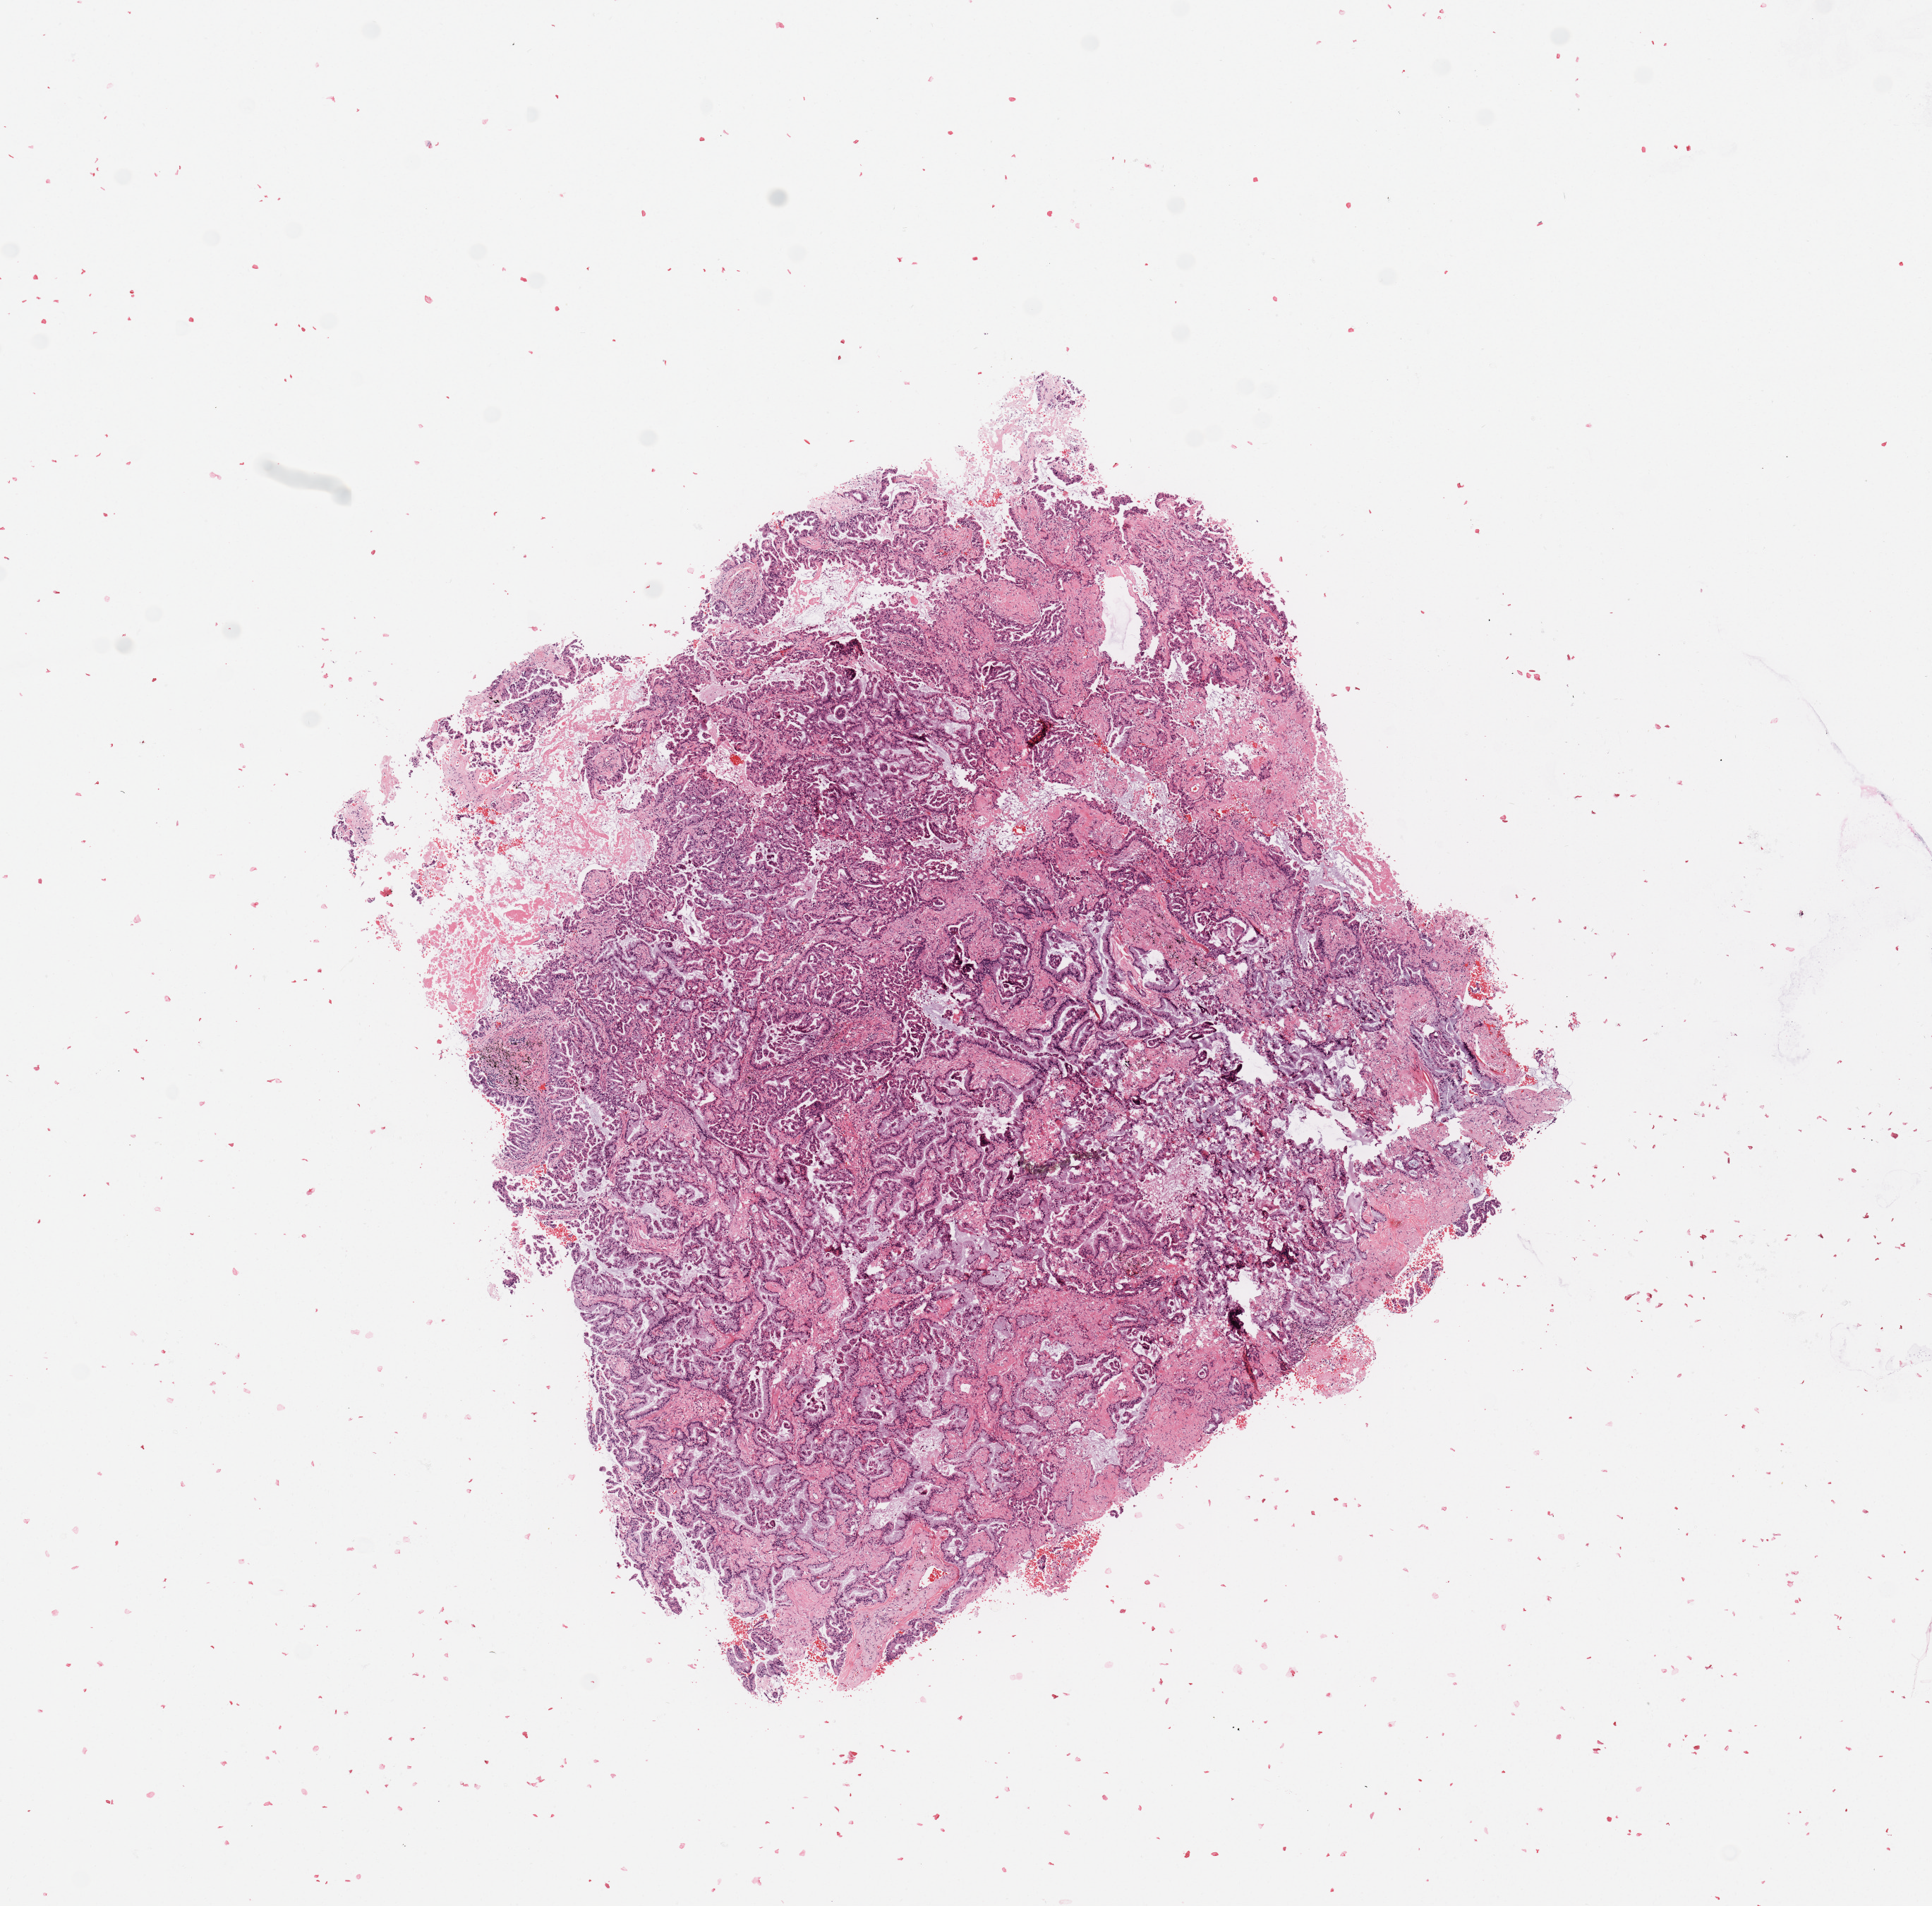
Whole-slide histology image, H&E, a low-resolution overview of the entire scanned area, about 10.8 x 10.7 mm (from a 20x scan); tumour tissue sample, sampled site: lung. Female, 56 y/o.
Histologic diagnosis: Adenocarcinoma, NOS.